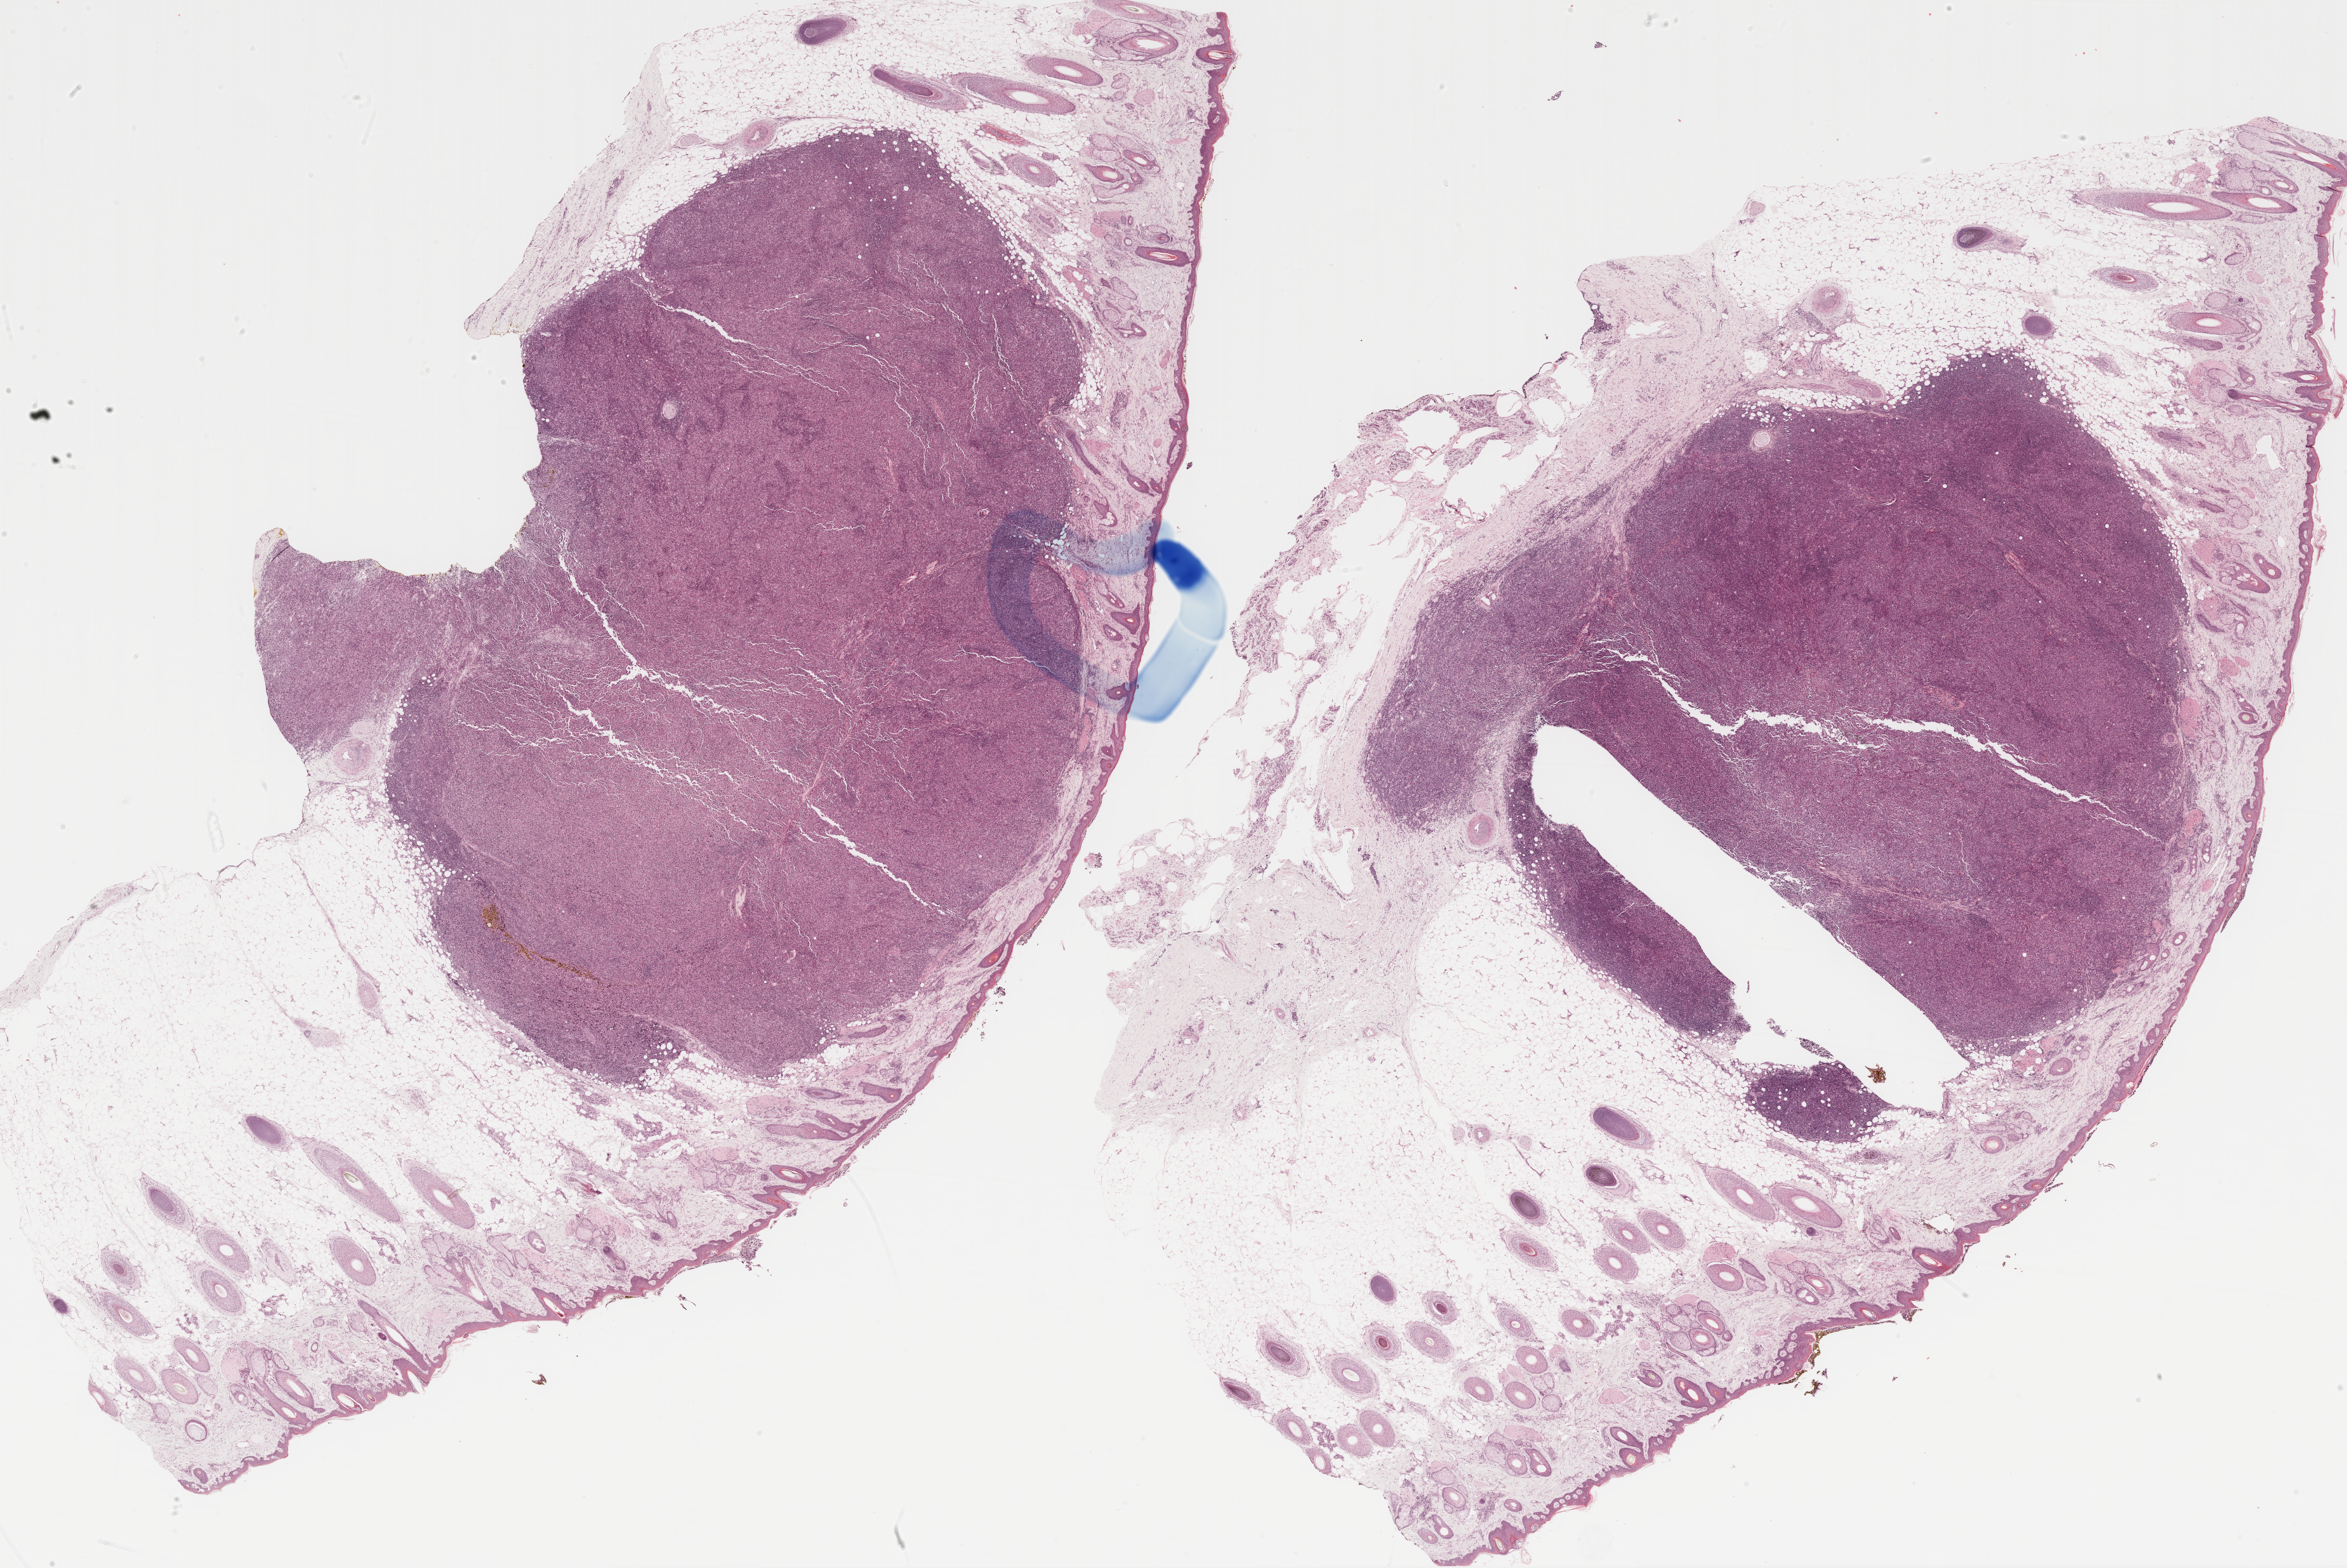
Digitized H&E-stained tissue section (whole slide) — shown as a low-resolution overview of the whole scanned area (about 29.8 x 19.9 mm, acquisition: 20x scan); formalin-fixed paraffin-embedded (FFPE) diagnostic section; metastatic tumour sample. Female patient; age at initial diagnosis 58 years.
This section: metastatic tumour tissue. Patient diagnosis: Malignant melanoma, NOS.